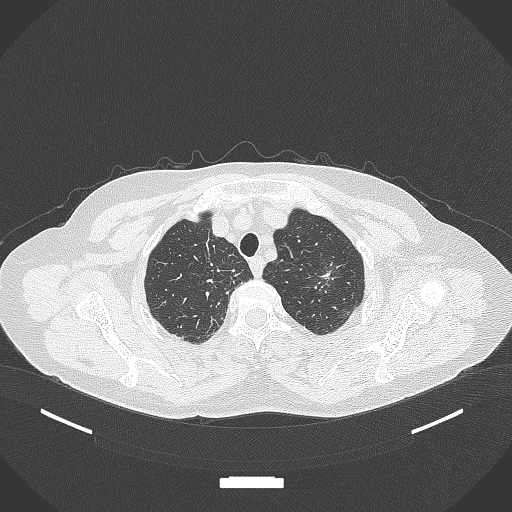
Chest CT, one axial slice; position 309 of 369 along the scan axis; reconstruction kernel B70f; 120 kVp; lung window (W 1500 / L -600 HU); 1 mm slice thickness; 512 × 512 image matrix, field of view 400 × 400 mm. Female patient, age 64 years. Case-level facts recorded for this patient, not image findings: clinical TNM (as recorded): T1c N0 M0; histopathological grade: G1.
Annotated regions visible in this slice (rectangle marked by the reading radiologist):
- lung tumour (recorded histology: adenocarcinoma): box from (x=305, y=248) to (x=345, y=302) px